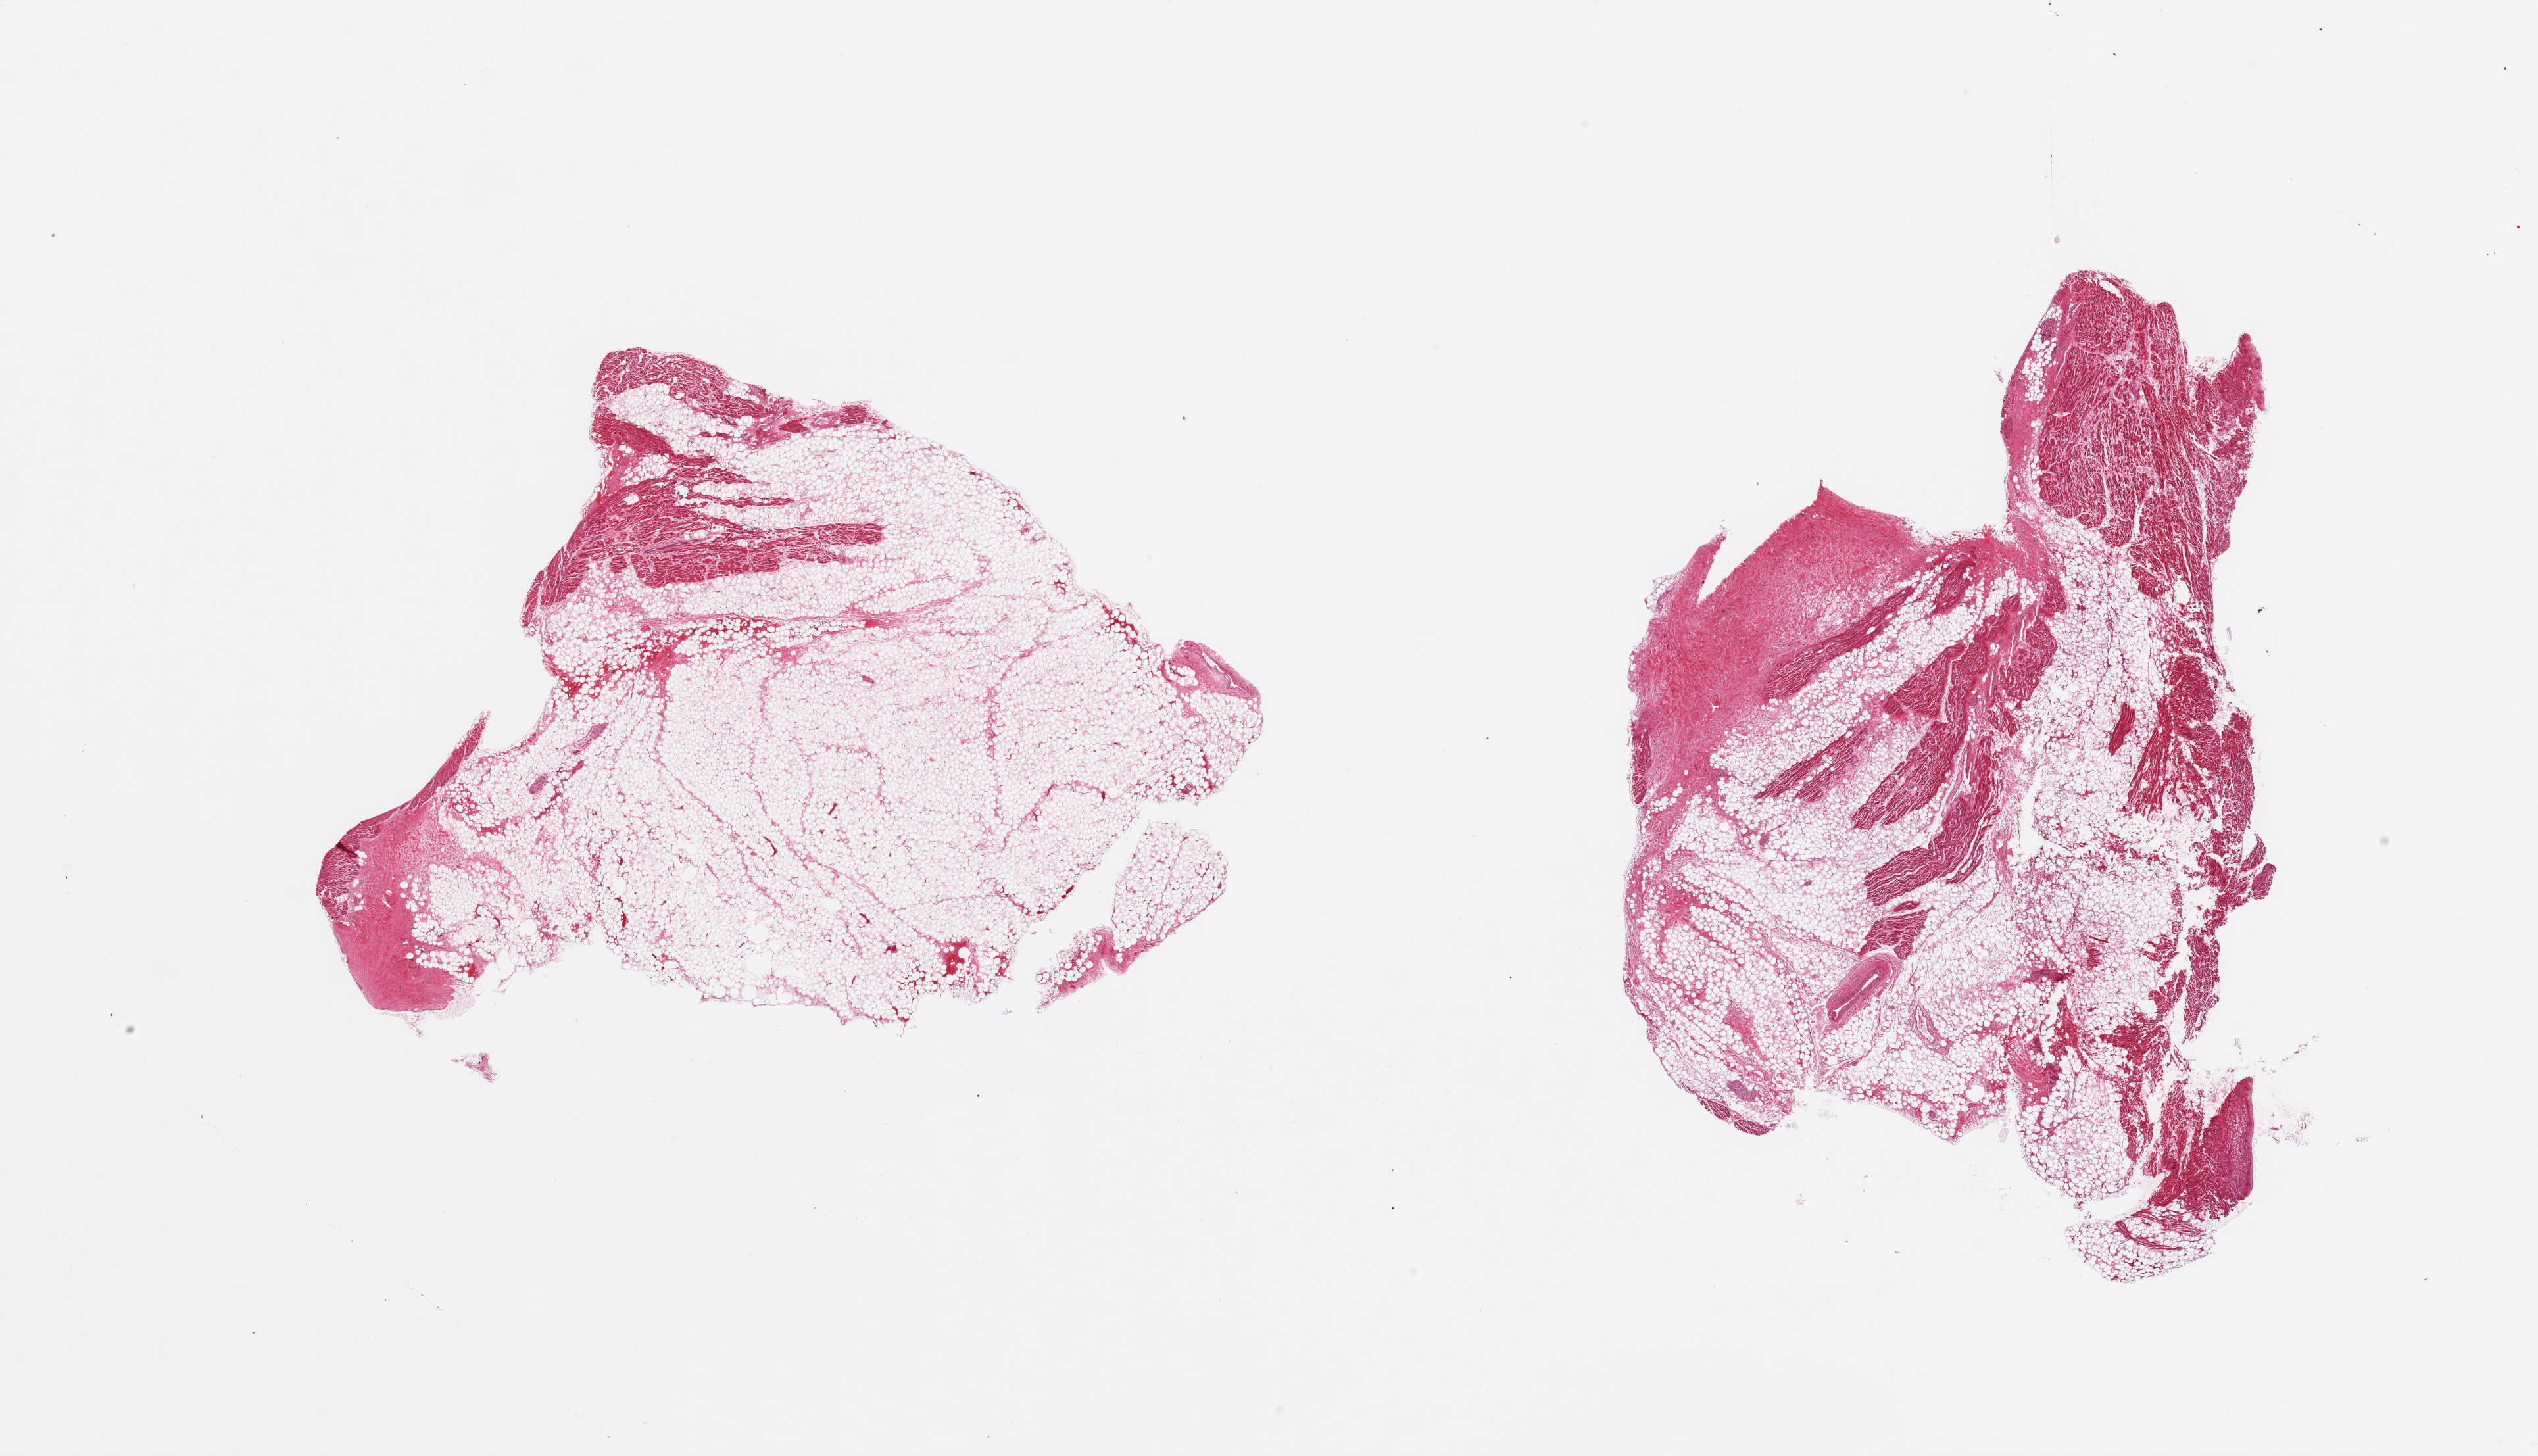
Whole-slide image, haematoxylin and eosin stain, brightfield, whole scanned area (about 30.5 x 17.5 mm) shown as a low-resolution overview. PAXgene-fixed, paraffin-embedded tissue. Section of auricular appendage (target tissue). Donor tissue sample. Donor: female.
Pathologist's review note for this sample: 2 pieces, no abnormalities, ~50% interstitial fat.